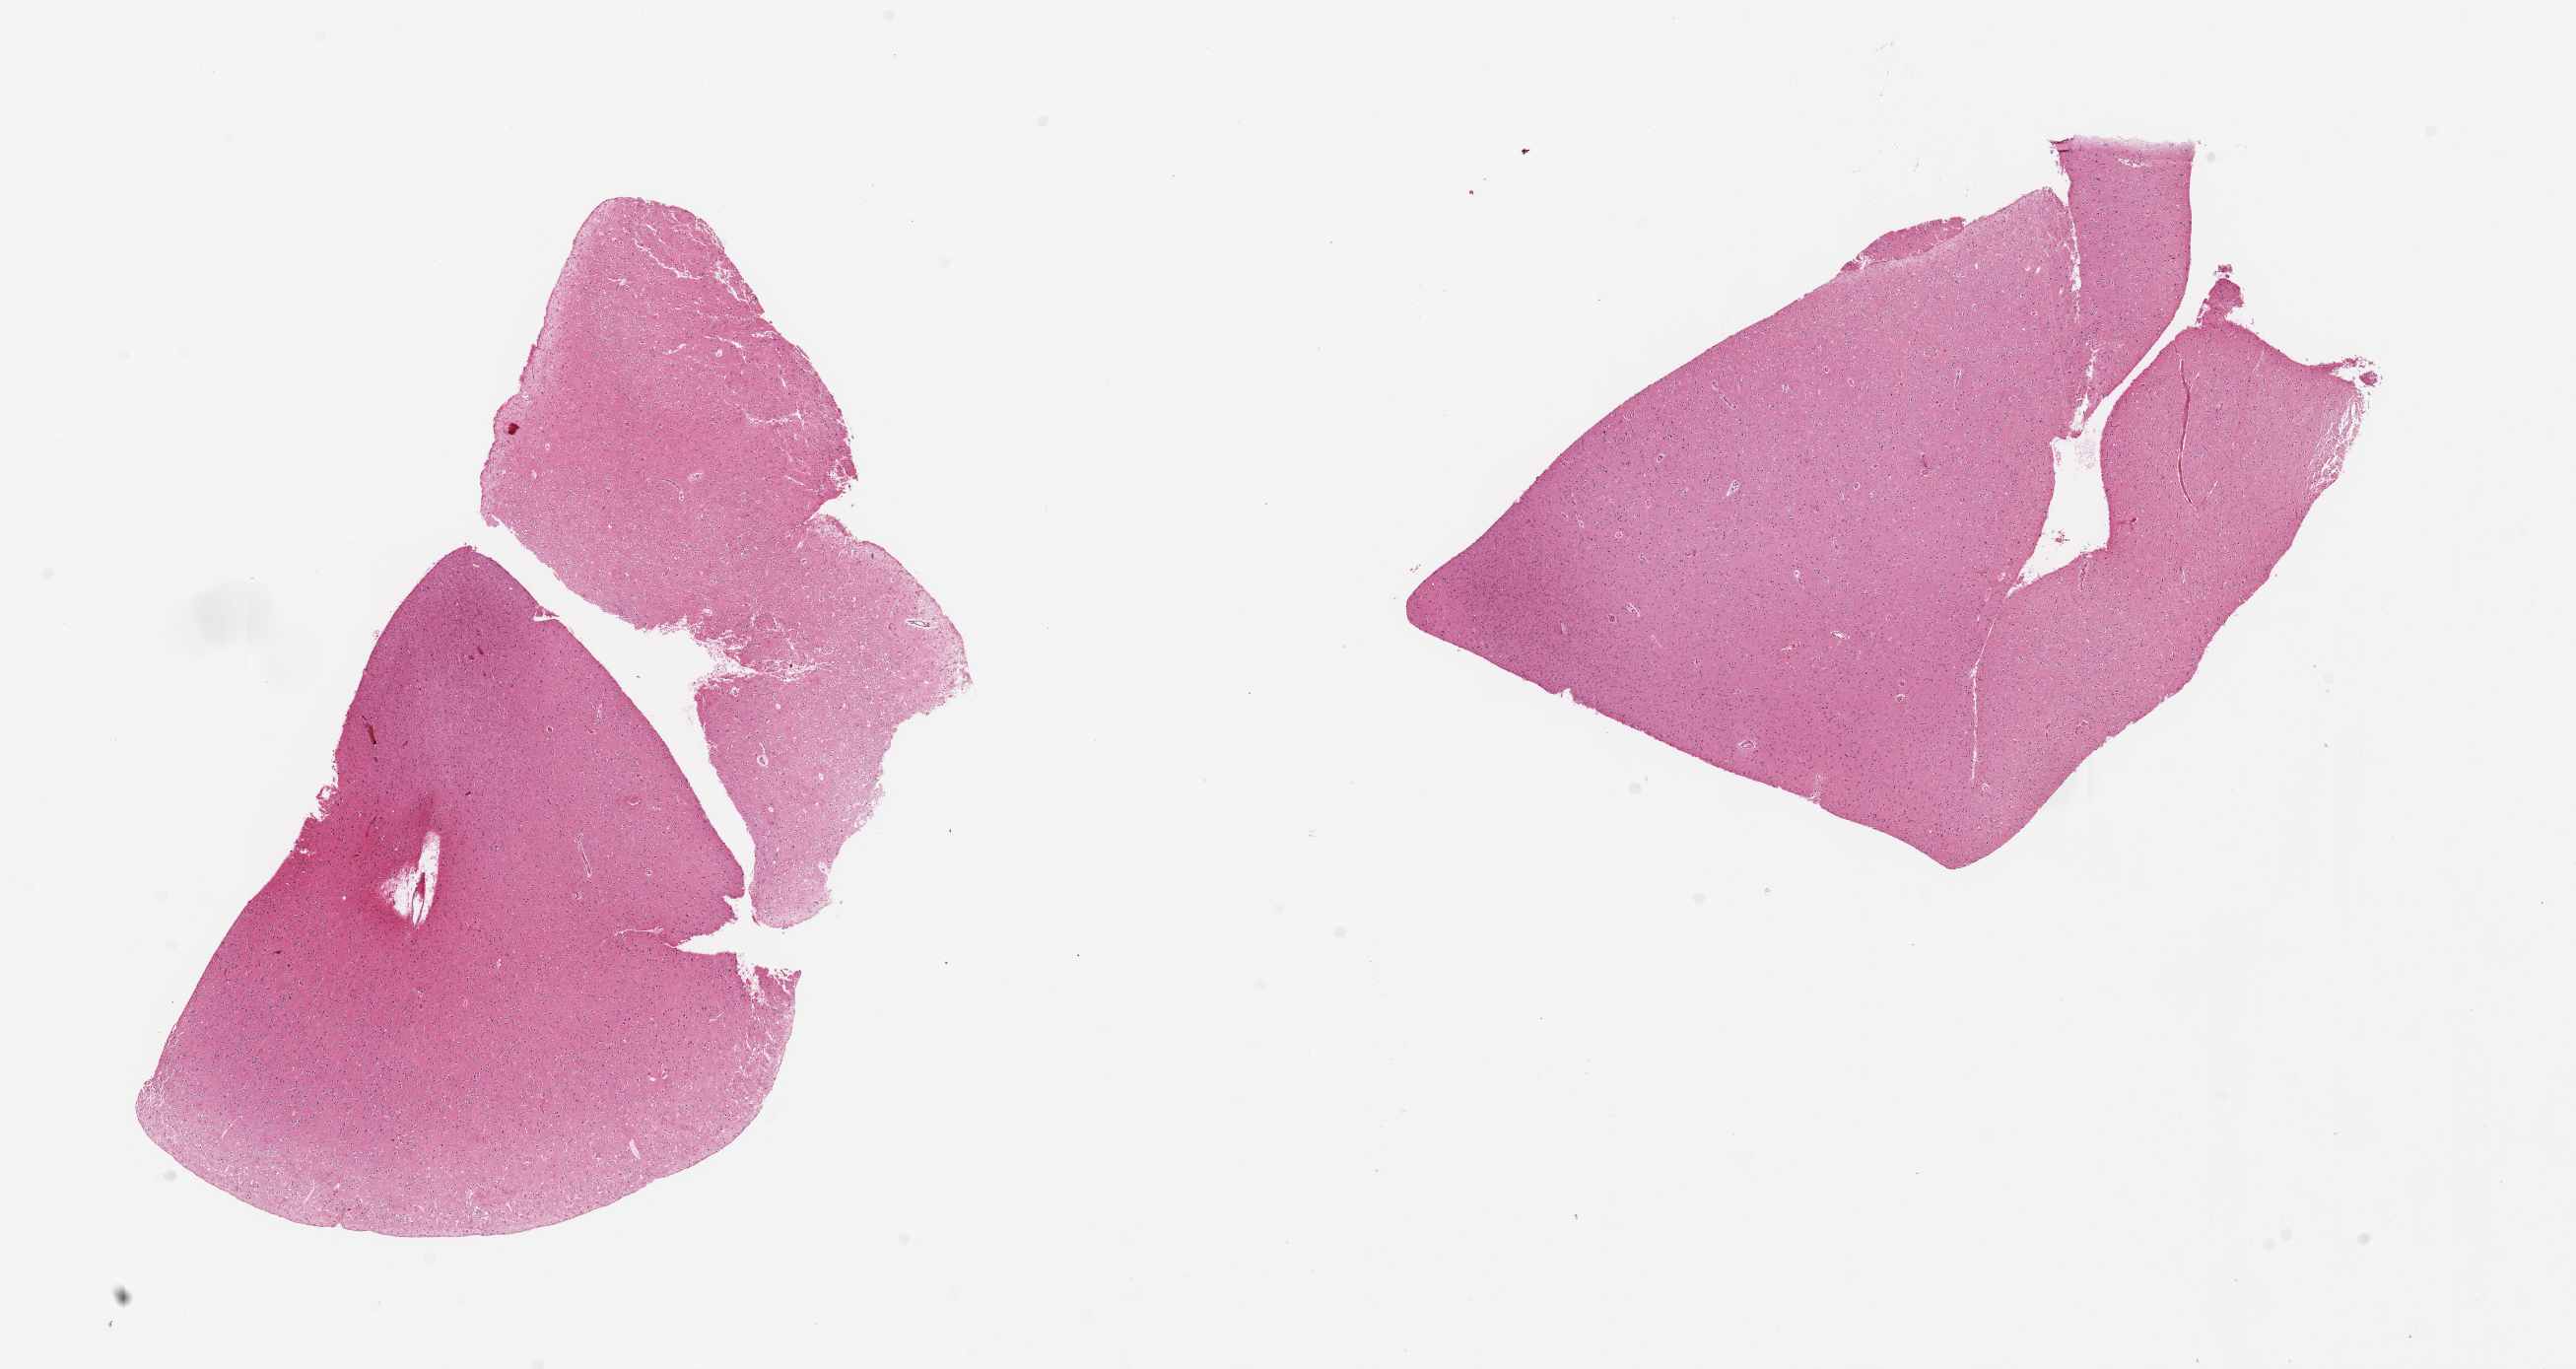
Hematoxylin and eosin (H&E) whole-slide image, a low-resolution overview of the entire scanned area, about 20.7 x 11.0 mm (from a 20x scan), PAXgene-fixed paraffin-embedded (PFPE) section, section of cerebral cortex (target tissue), donor tissue sample. Male donor.
Review note (as recorded): 2 pieces no abnormalities.